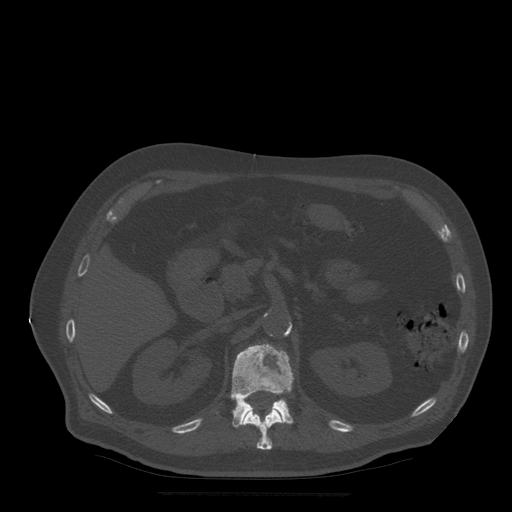
CT including the spine, one axial slice; position 205 of 522 along the scan axis; bone window (W 1800 / L 400 HU); 1.25 mm slice thickness; 512 × 512 image matrix, field of view 420 × 420 mm. Patient age 72 years. From the clinical record (not read from this slice): primary cancer: prostate.
Structures marked on this image (semi-automatic segmentation, software-assisted and operator-edited):
- L1 vertebra: box from (x=231, y=344) to (x=294, y=428) px
- T12 vertebra: (x=244, y=409)–(x=283, y=450)